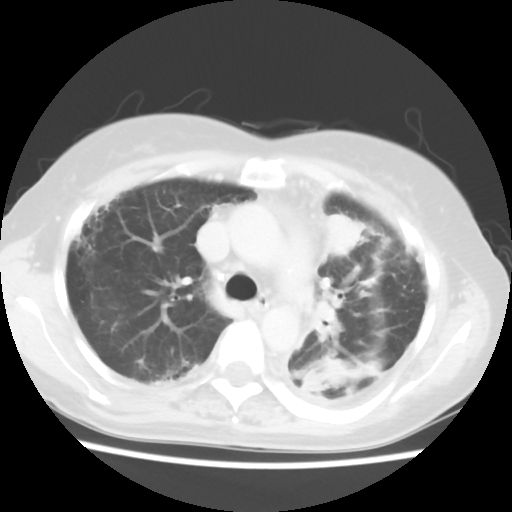
Chest CT, one axial slice; position 39 of 56 along the scan axis; 120 kVp; lung window (W 1500 / L -600 HU); 5 mm slice thickness; 512 × 512 image matrix, field of view 309 × 309 mm. Patient: female, 56 years. Case-level facts recorded for this patient, not image findings: clinical TNM (as recorded): T1c N0 M1.
Outlined on this slice (bounding box drawn by a radiologist):
- lung tumour (recorded histology: adenocarcinoma): bounding box [x1, y1, x2, y2] px = [323, 207, 374, 269]